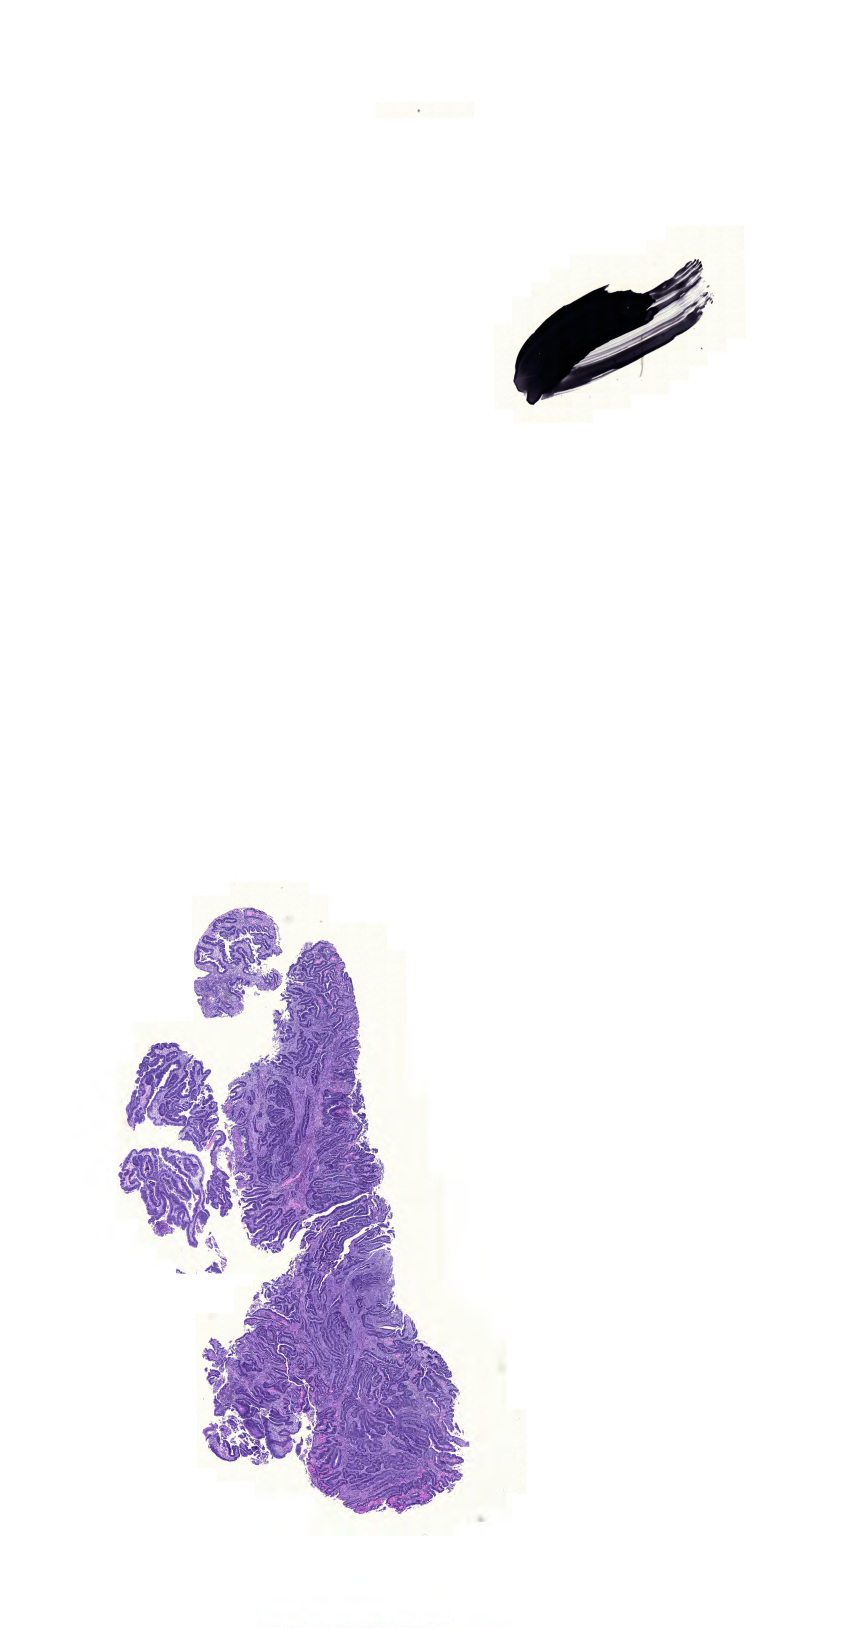
Whole-slide histology image, H&E — a low-resolution overview of the entire scanned area, about 12.7 x 24.2 mm (from a 20x scan). Formalin-fixed paraffin-embedded (FFPE) diagnostic section. Sample: primary tumour, rectum. Female patient; age at initial diagnosis 67 years.
- AJCC pathologic stage: I (6th edition)
- histologic diagnosis: Adenocarcinoma, NOS
- lymph nodes positive (case pathology): 0 of 26 examined
- TNM: T2 N0 M0